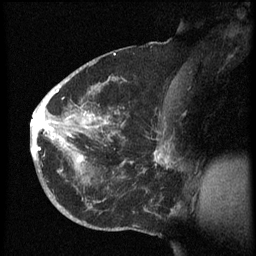
Breast MRI (dynamic contrast-enhanced), one sagittal slice; slice 34 of 60 in the series (ordered by position); dynamic contrast-enhanced series, image 2 of 3 at this slice position (ordered by acquisition); 1.5 T; TE 4.2 ms, TR 8.4 ms; 256 × 256 image matrix, field of view 200 × 200 mm. Patient: female, 38 years. From the clinical record (not read from this slice): setting: breast cancer imaged before/during neoadjuvant chemotherapy; receptor status: HER2-positive.
Outlined on this slice (semi-automatic segmentation, software-assisted and operator-edited):
- analysis volume of interest (the breast-tissue region the enhancement analysis was run in; not a lesion): bounding box (x1, y1, x2, y2) in pixels: (31, 74, 173, 202)
- tumour enhancement mask (voxels above the 70 % enhancement threshold inside the analysis volume of interest): (31, 90, 171, 165)